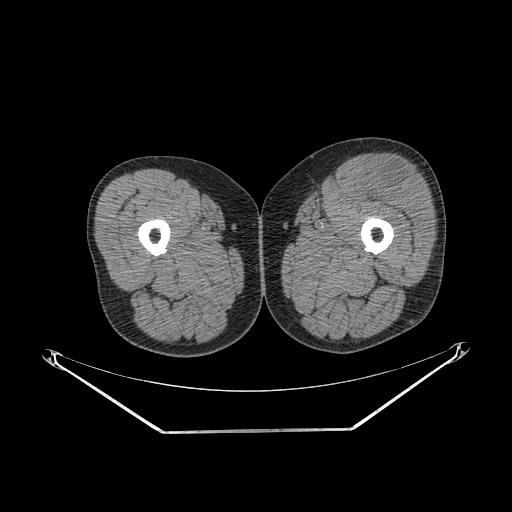
CT of an extremity soft-tissue mass (from a PET/CT study), one axial slice. Position 226 of 267 along the scan axis. Reconstruction kernel SOFT. 140 kVp. Soft-tissue window (W 400 / L 40 HU). 3.75 mm slice thickness. 512 × 512 image matrix, field of view 500 × 500 mm. Male patient. Case-level facts recorded for this patient, not image findings: histological type: extraskeletal osteosarcoma; grade: high; site of the primary tumour: thigh.
Annotated regions visible in this slice (expert contour drawn on MRI and transferred to this co-registered scan by the dataset authors):
- gross tumour volume (mass): bounding box <368,164,421,209> (left, top, right, bottom; pixels)